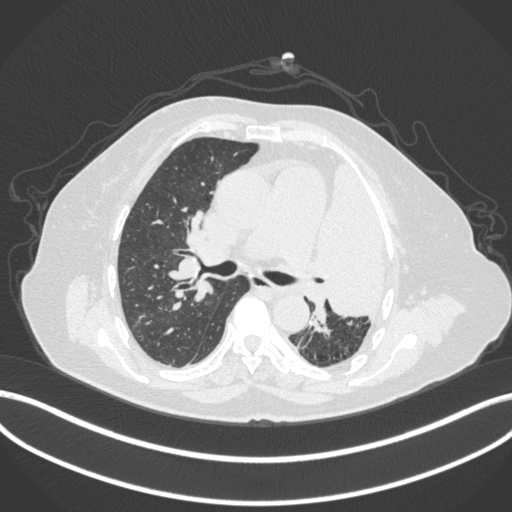
Chest CT, one axial slice; position 237 of 399 along the scan axis; reconstruction kernel B31f; lung window (W 1500 / L -600 HU); 512 × 512 image matrix, field of view 400 × 400 mm. Female patient, age 75 years. Case-level facts recorded for this patient, not image findings: clinical TNM (as recorded): T3 N3 M1.
Structures marked on this image (rectangle marked by the reading radiologist):
- lung tumour (recorded histology: adenocarcinoma): box from (x=316, y=153) to (x=399, y=324) px